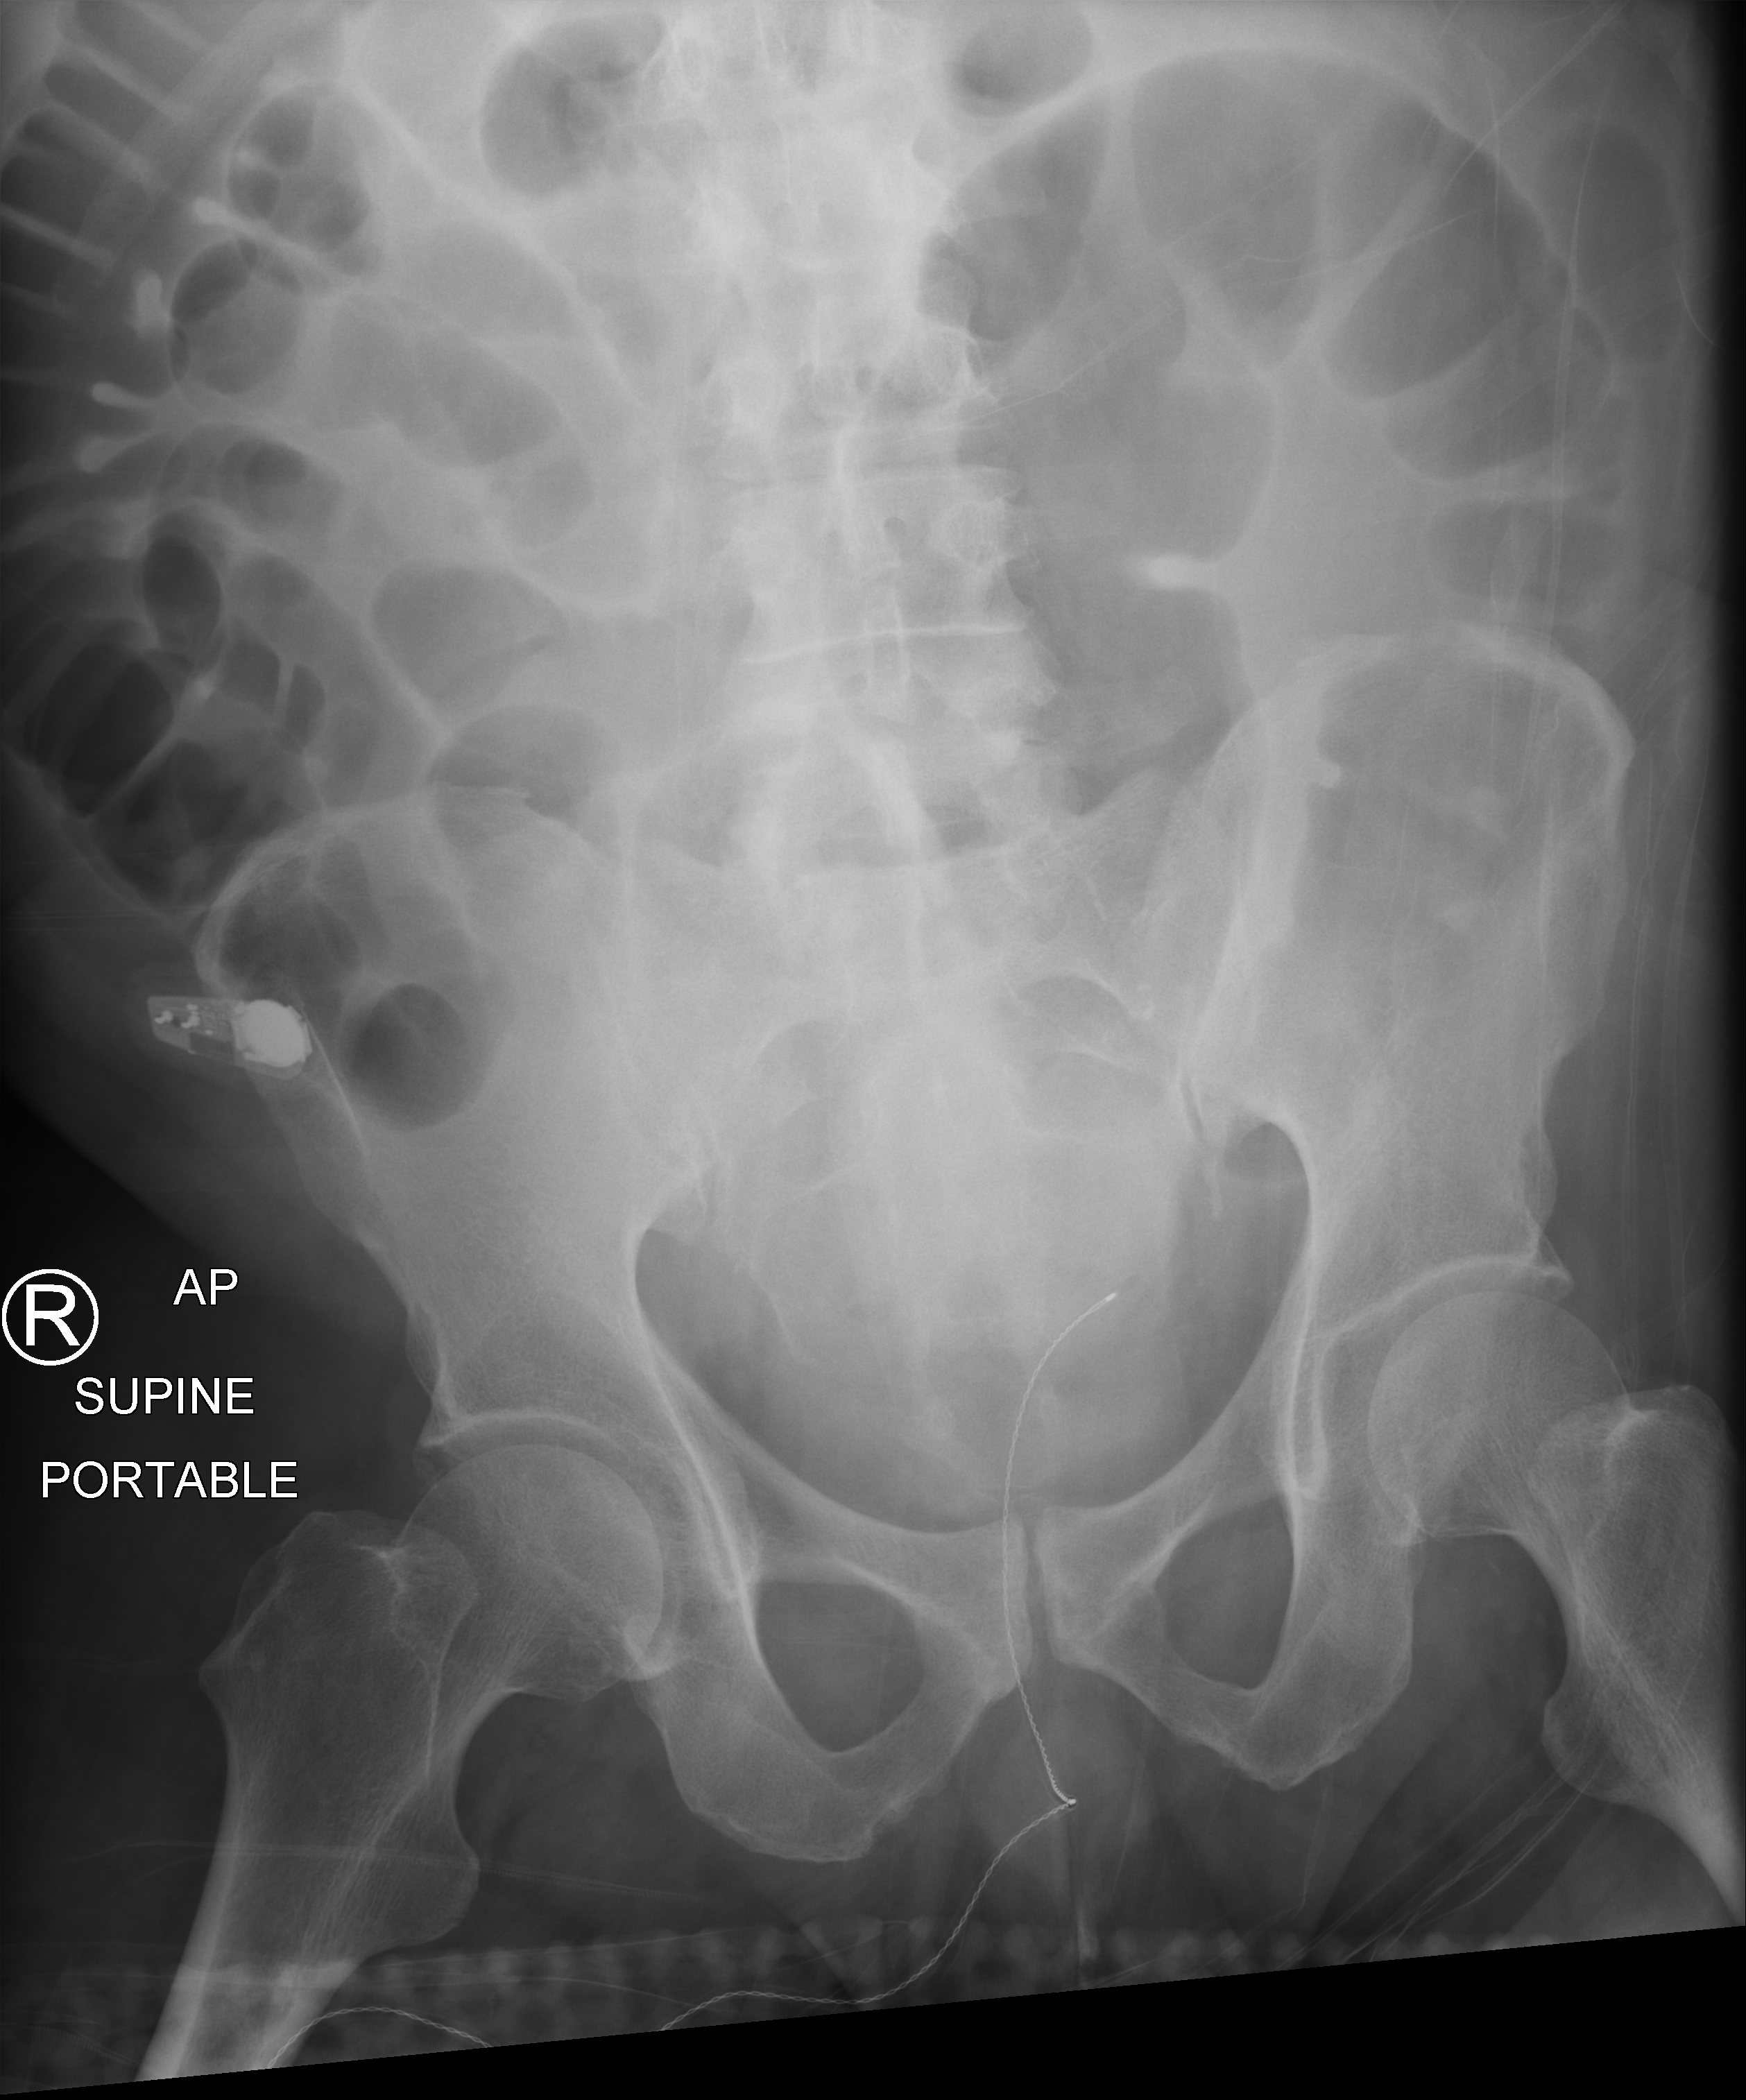
Portable abdomen radiograph; anteroposterior (AP) projection. Patient hospitalised with COVID-19; male, aged 18–59 years.
Admission-level facts for this patient (not findings on this image; timing relative to this image not recorded):
- mechanically ventilated during this hospital stay: yes
- length of hospital stay: 63 days
- chronic kidney disease (admission record): no